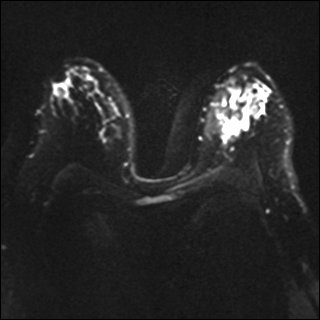
Breast MRI, one axial slice; position 23 of 37 along the scan axis; diffusion-weighted series; image 2 of 4 stored at this slice position (different b-values; order by instance number); 1.5 T; 4 mm slice thickness; 320 × 320 image matrix, field of view 340 × 340 mm. Female patient.
Outlined on this slice (outlined manually by an expert reader):
- tumour on diffusion-weighted imaging: bounding box [x1, y1, x2, y2] px = [226, 117, 247, 133]